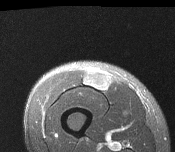
MRI of an extremity soft-tissue mass, one axial slice. Position 39 of 116 along the scan axis. T2-weighted fat-saturated. MR volume resampled by the dataset authors to the PET/CT grid (not the native acquisition matrix). 3.27 mm slice thickness. 175 × 152 image matrix, field of view 171 × 148 mm. Male patient. Case-level facts recorded for this patient, not image findings: histological type: pleiomorphic leiomyosarcoma; grade: intermediate; site of the primary tumour: right thigh.
Structures marked on this image (expert contour drawn on MRI and transferred to this co-registered scan by the dataset authors):
- gross tumour volume including surrounding oedema: box from (x=85, y=72) to (x=110, y=89) px